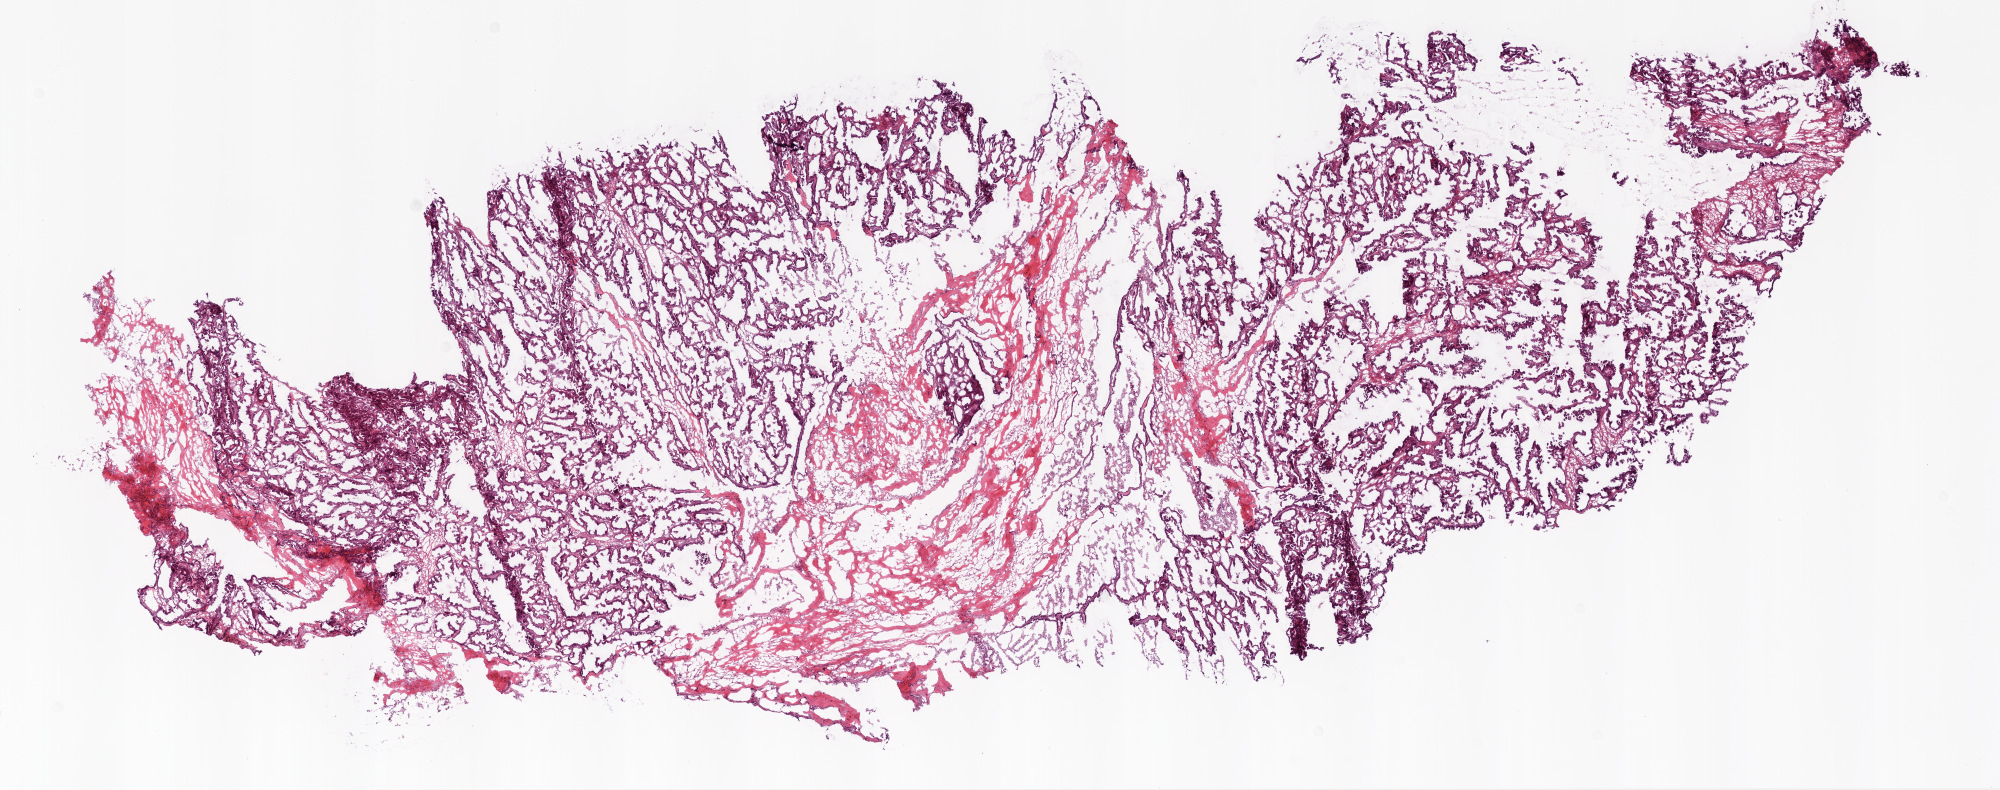
Whole-slide histology image, Hematoxylin and eosin (H&E) stained — shown as a low-resolution overview of the whole scanned area (about 16.0 x 6.3 mm). Frozen section. Primary tumour sample from the ovary. Female, age 74 years at initial diagnosis. Histologic grade: G3 (poorly differentiated). Slide review estimates, as recorded: tumour cells 85%, tumour nuclei 75%, normal cells 0%, stromal cells 15%, necrosis 0%. Inflammatory infiltration, as recorded: monocyte infiltration 3%.
- diagnosis: Serous cystadenocarcinoma, NOS
- FIGO stage: IIIC